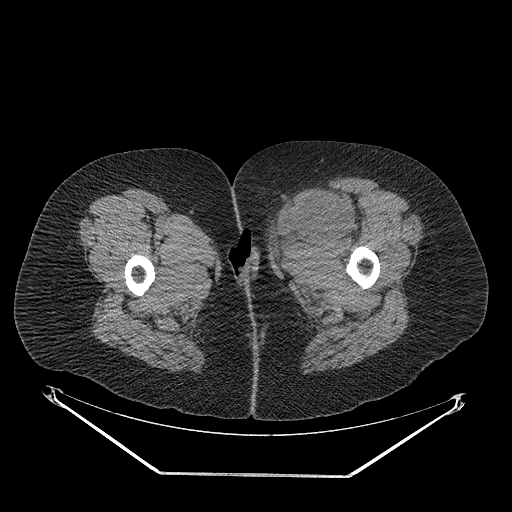
CT of an extremity soft-tissue mass (from a PET/CT study), one axial slice; position 37 of 267 along the scan axis; 140 kVp; soft-tissue window (W 400 / L 40 HU); 3.75 mm slice thickness; 512 × 512 image matrix, field of view 500 × 500 mm. Female patient. Case-level facts recorded for this patient, not image findings: histological type: myxofibrosarcoma; grade: intermediate; site of the primary tumour: left thigh.
Outlined on this slice (expert contour drawn on MRI and transferred to this co-registered scan by the dataset authors):
- gross tumour volume including surrounding oedema: bounding box <267,190,359,257> (left, top, right, bottom; pixels)
- gross tumour volume (mass): <272,190,350,243>